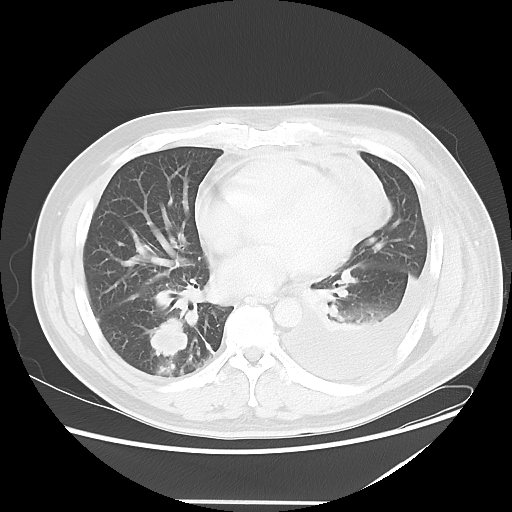
Chest CT, one axial slice. Position 21 of 52 along the scan axis. 120 kVp. Lung window (W 1500 / L -600 HU). 5 mm slice thickness. 512 × 512 image matrix. Patient: male, 42 years. From the clinical record (not read from this slice): clinical TNM (as recorded): T2 N1 M1.
Annotated regions visible in this slice (rectangle marked by the reading radiologist):
- lung tumour (recorded histology: adenocarcinoma): bounding box <142,315,192,361> (left, top, right, bottom; pixels)